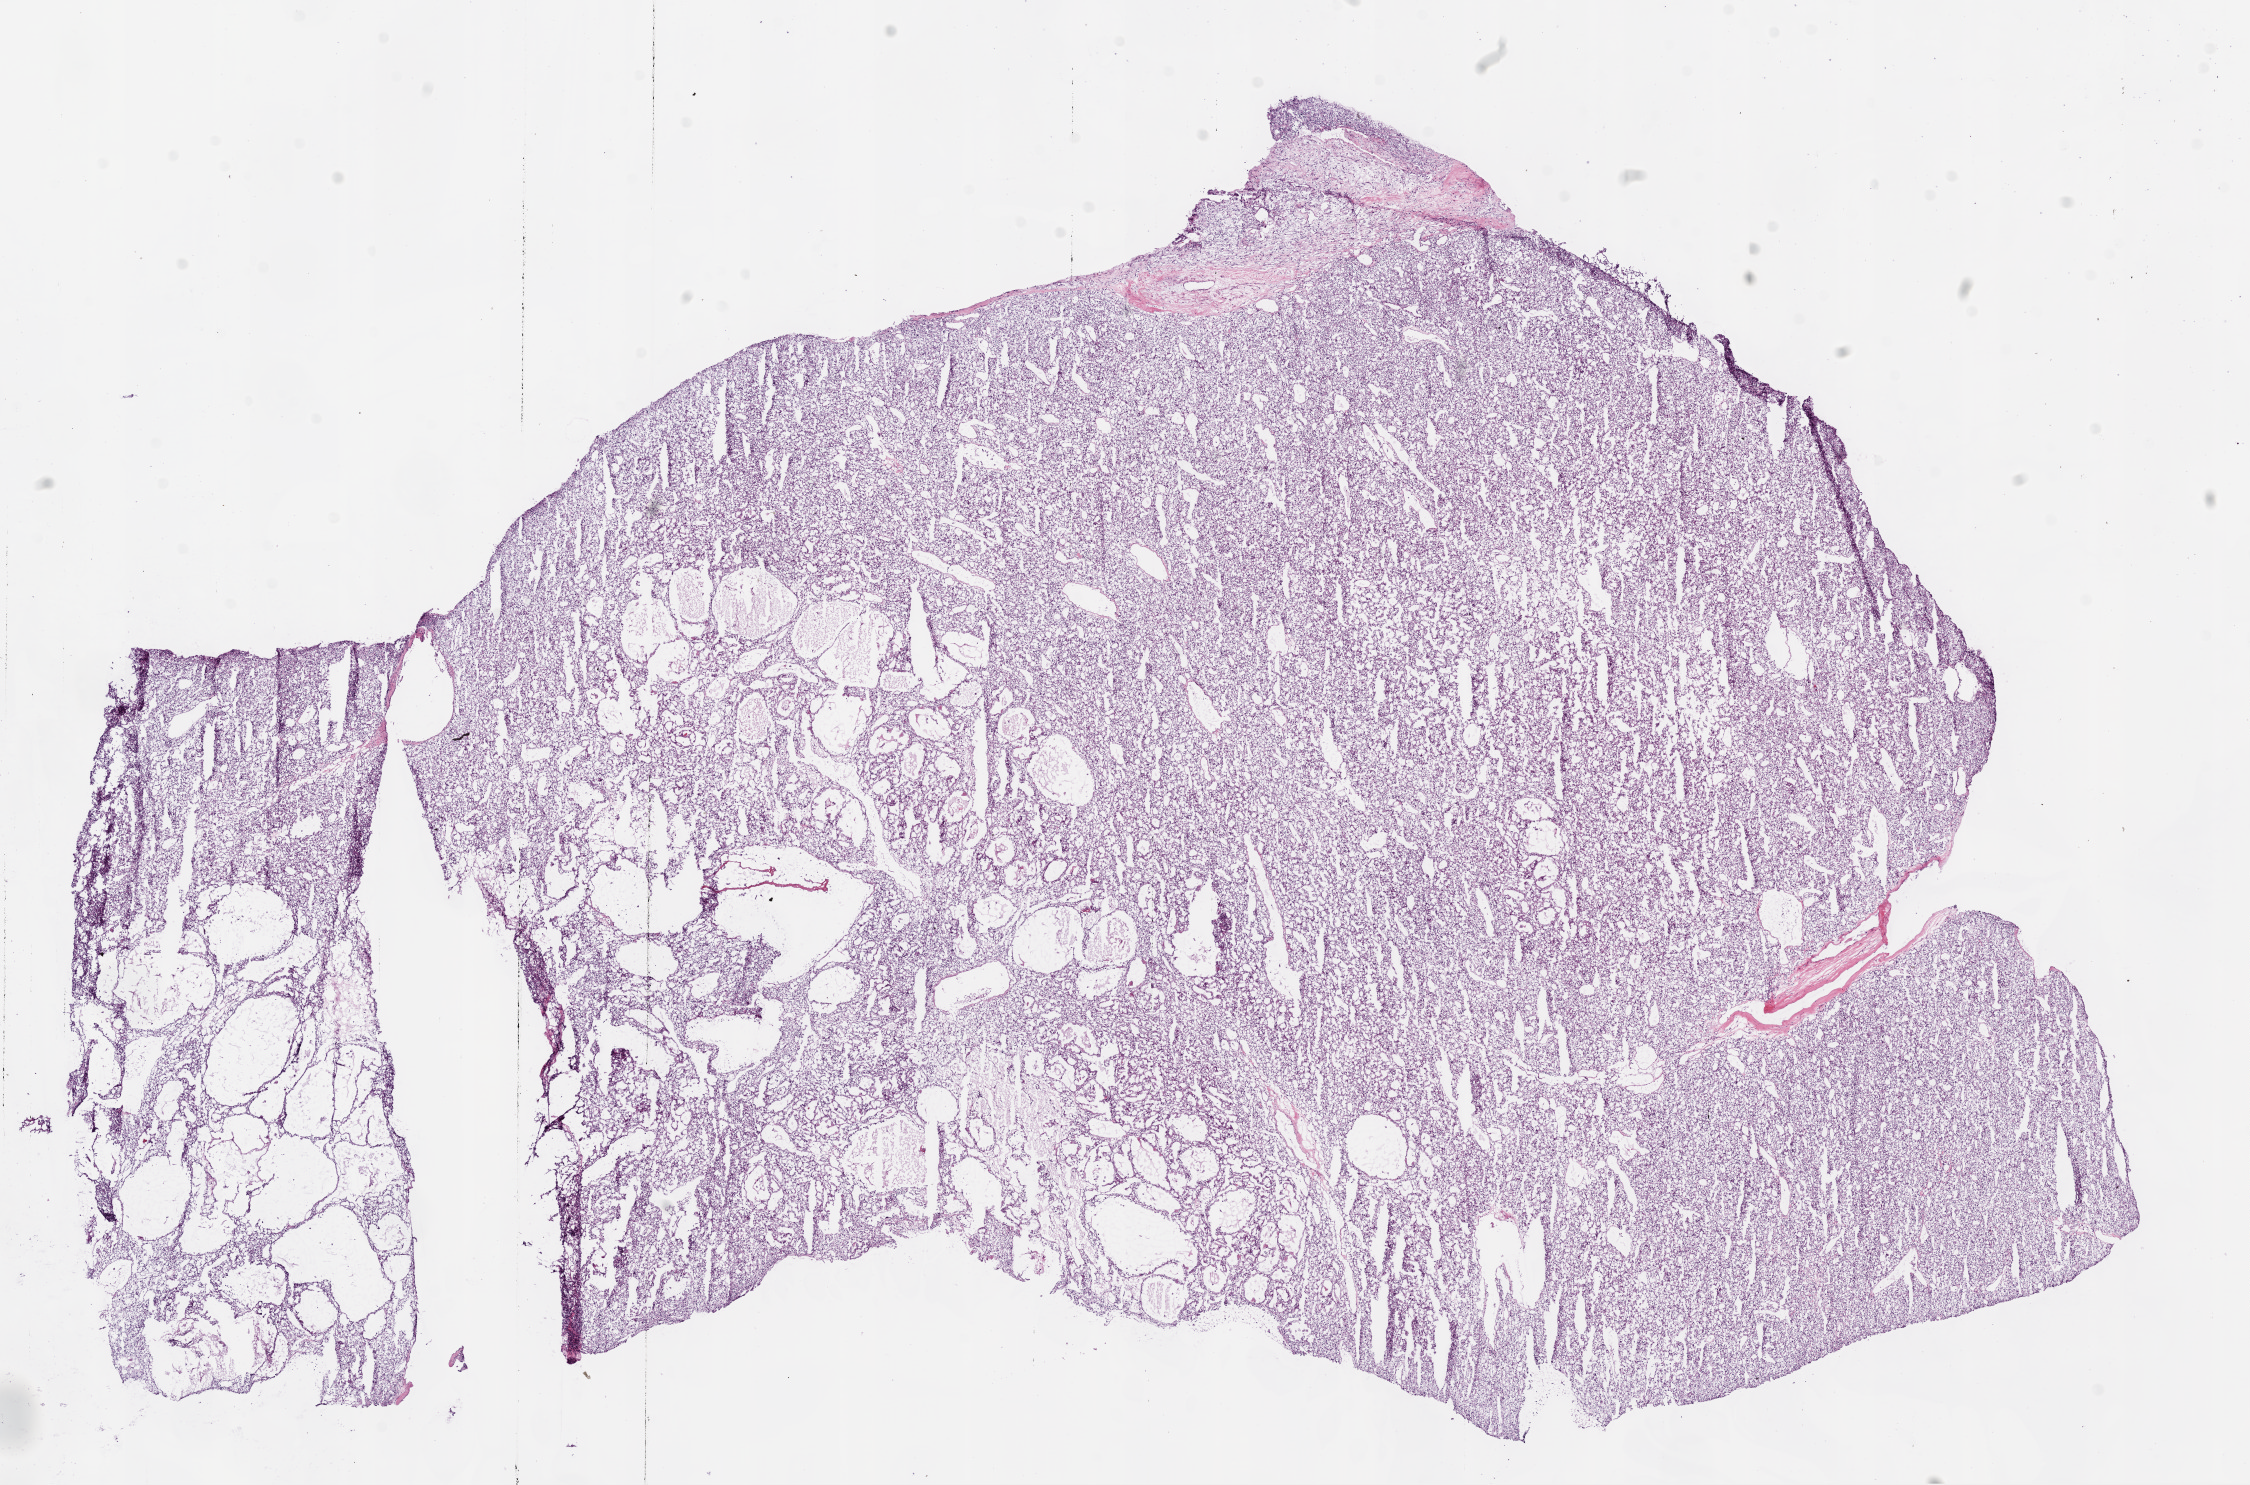
Whole-slide histology image, H&E-stained — a low-resolution overview of the entire scanned area, about 18.1 x 11.9 mm. Frozen section. Sample: primary tumour, kidney. Male, age 67 years at initial diagnosis. Histologic grade: G2 (moderately differentiated). Slide review estimates, as recorded: tumour cells 95%, tumour nuclei 85%, normal cells 0%, stromal cells 5%, necrosis 0%.
TNM: T3a NX M0. AJCC pathologic stage: III. Histologic diagnosis: Clear cell adenocarcinoma, NOS.